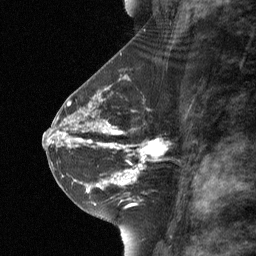
Breast MRI (dynamic contrast-enhanced), one sagittal slice; position 33 of 64 along the scan axis; dynamic contrast-enhanced study with each time point stored as its own series, time point 2 of 3 at this slice position (early post-contrast, ordered by acquisition time); 1.5 T; TE 4.8 ms, TR 27 ms; 2 mm slice thickness; 256 × 256 image matrix, field of view 180 × 180 mm. Female patient, age 42 years. Case-level facts recorded for this patient, not image findings: setting: breast cancer imaged before/during neoadjuvant chemotherapy; receptor status: triple-negative.
Annotated regions visible in this slice (semi-automatically segmented with operator editing):
- analysis volume of interest (the breast-tissue region the enhancement analysis was run in; not a lesion): bounding box [x1, y1, x2, y2] px = [111, 125, 163, 178]
- tumour enhancement mask (voxels above the 90 % enhancement threshold inside the analysis volume of interest): [111, 131, 157, 178]